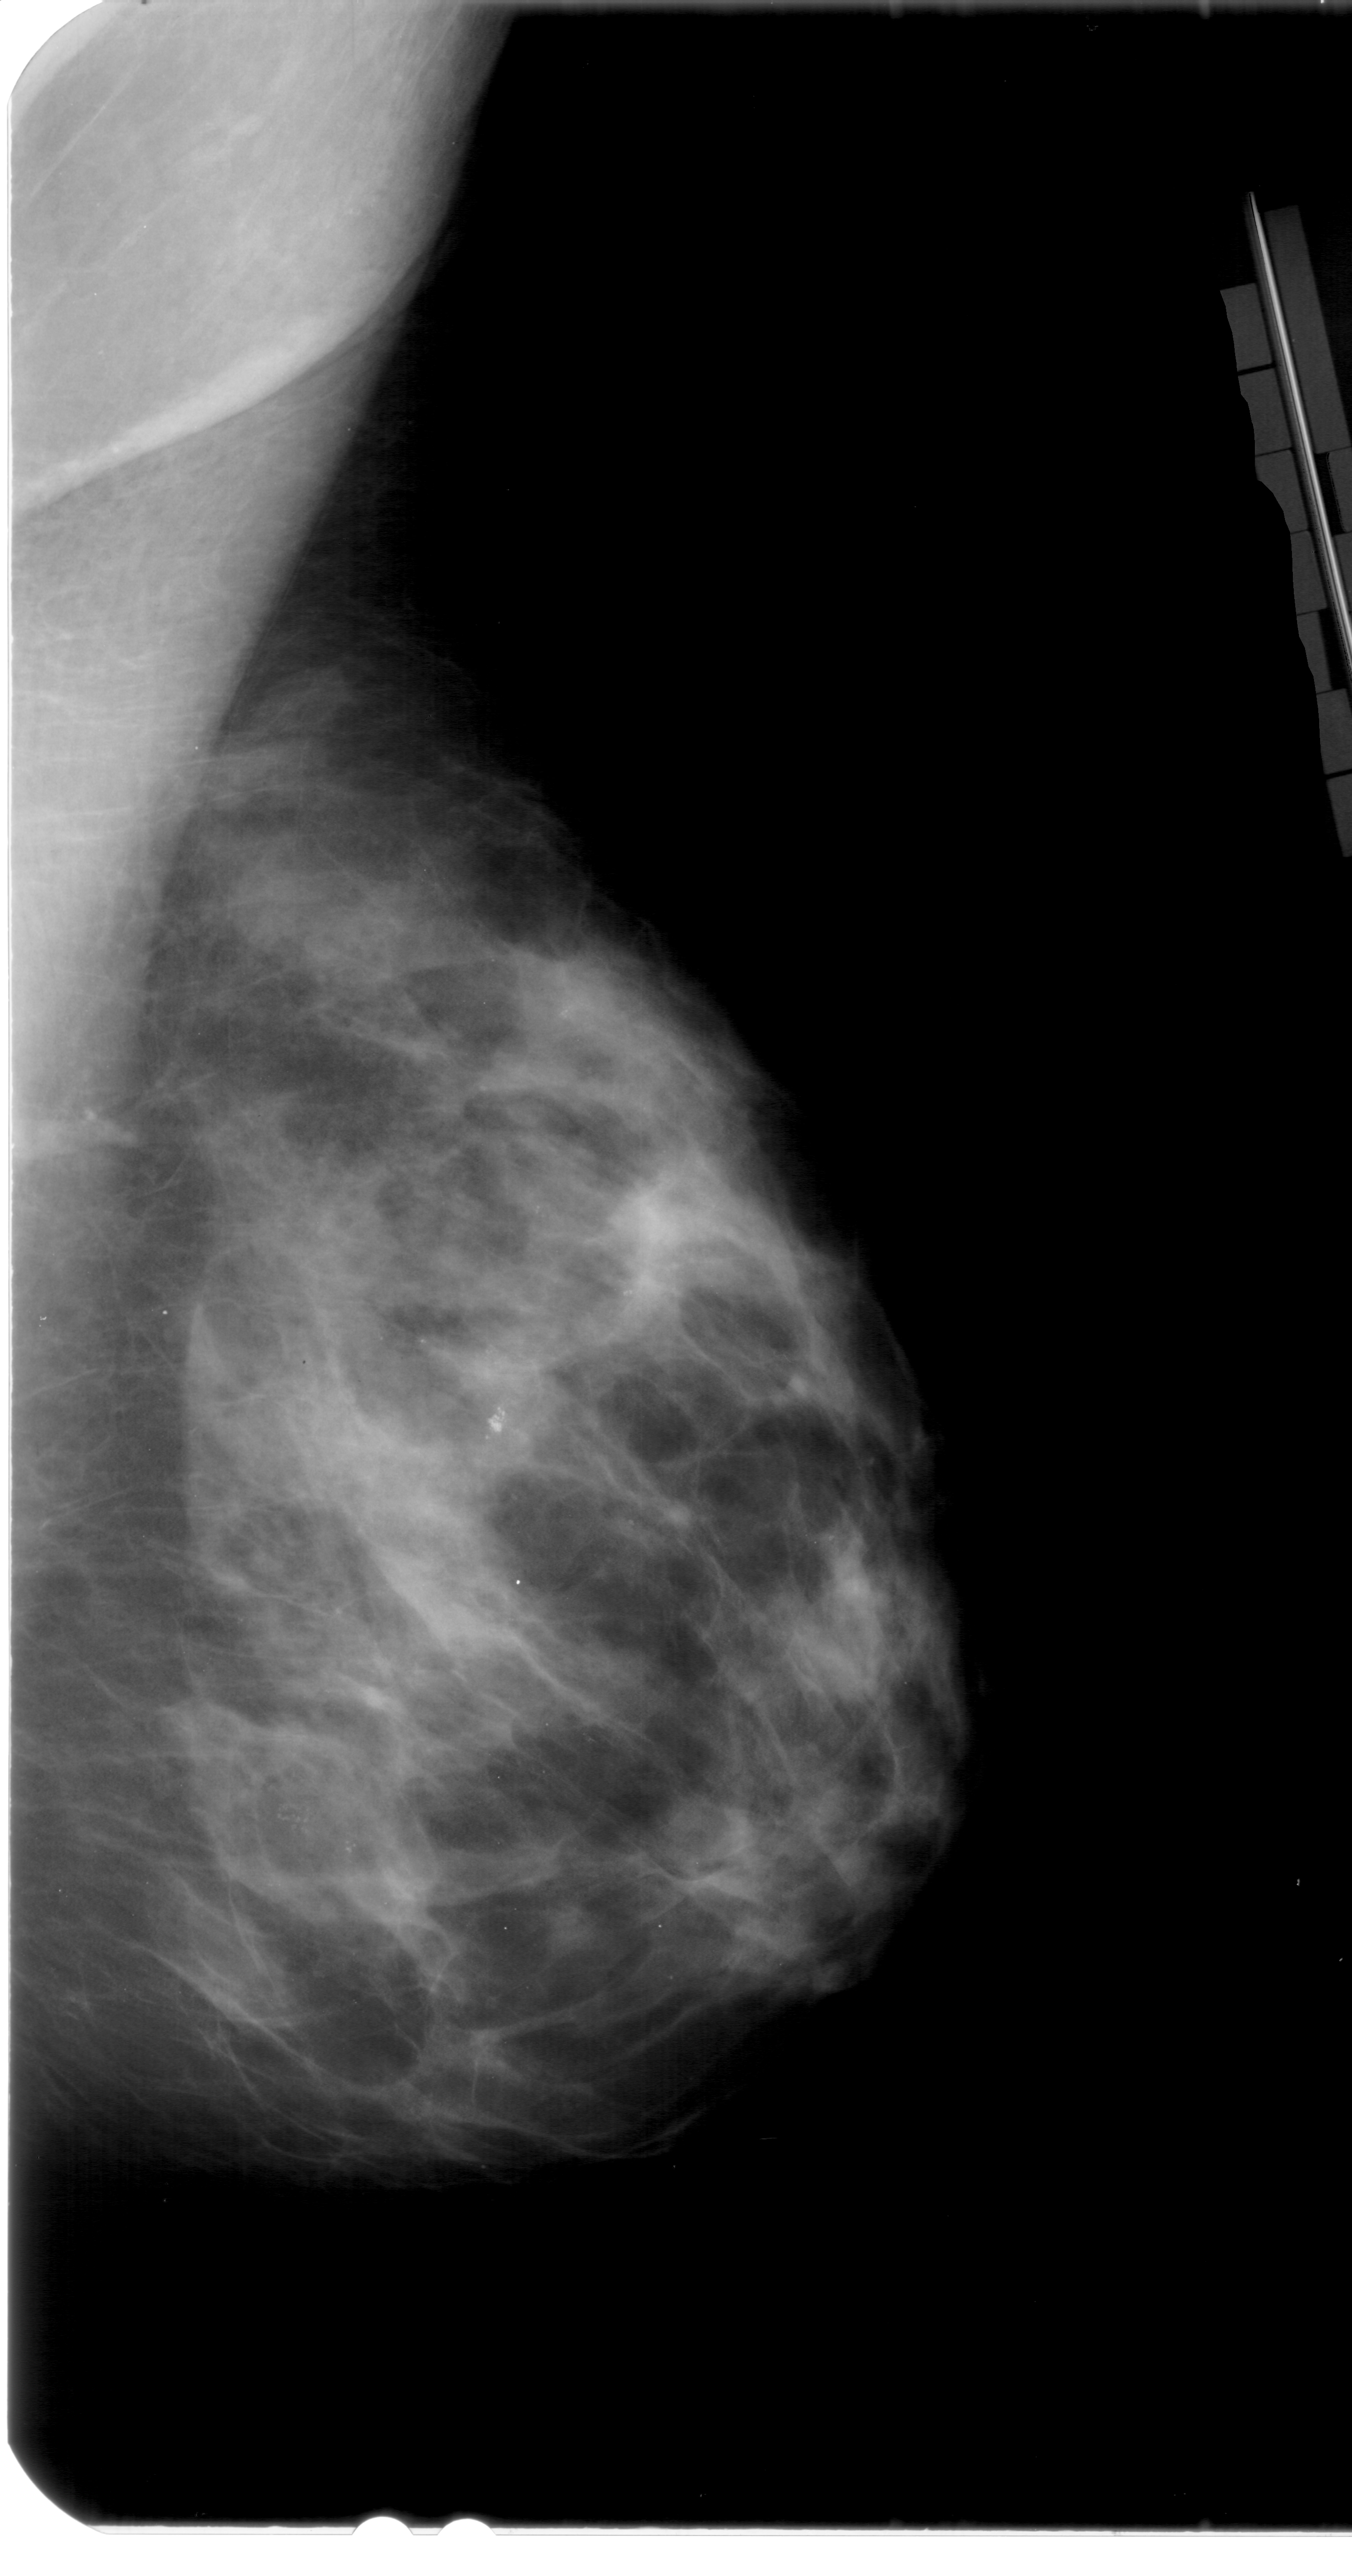
Digitized screen-film mammogram, right breast, MLO view, breast composition: extremely dense (BI-RADS density category 4 of 4).
Calcifications, morphology pleomorphic, distribution clustered; BI-RADS assessment category 4; pathology result (as recorded, not read from the image): benign.